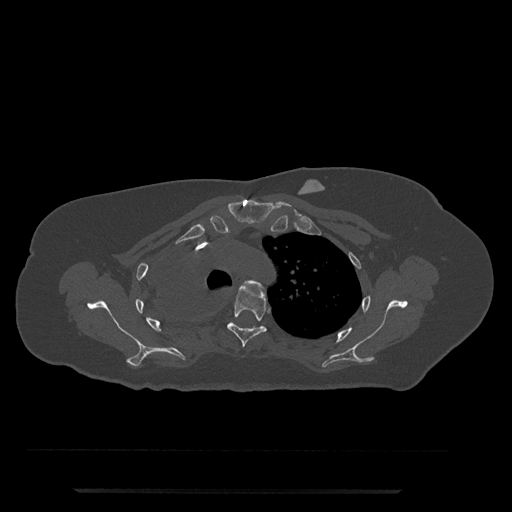
CT including the spine, one axial slice; position 590 of 797 along the scan axis; reconstruction kernel Br40s/3; bone window (W 1800 / L 400 HU); 0.5 mm slice thickness; 512 × 512 image matrix, field of view 440 × 440 mm. Patient: female, 51 years. Case-level facts recorded for this patient, not image findings: primary cancer: neuro.
Annotated regions visible in this slice (semi-automatic segmentation, software-assisted and operator-edited):
- T3 vertebra: bounding box <242,280,264,290> (left, top, right, bottom; pixels)
- T4 vertebra: <227,286,267,348>
- T5 vertebra: <233,323,258,328>